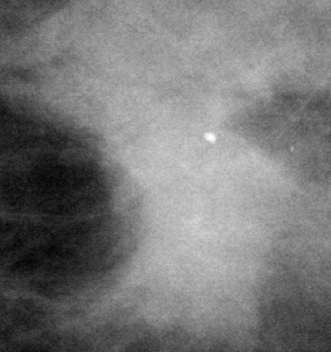
Cropped region of a digitized screen-film mammogram centred on a radiologist-marked abnormality; left breast; CC view; BI-RADS breast density category 3 (scale 1–4).
- Marked abnormality: mass, shape irregular, margins ill defined; BI-RADS assessment category 5; subtlety rating 4 on a 1 (subtle) to 5 (obvious) scale; pathology result (as recorded, not read from the image): malignant.